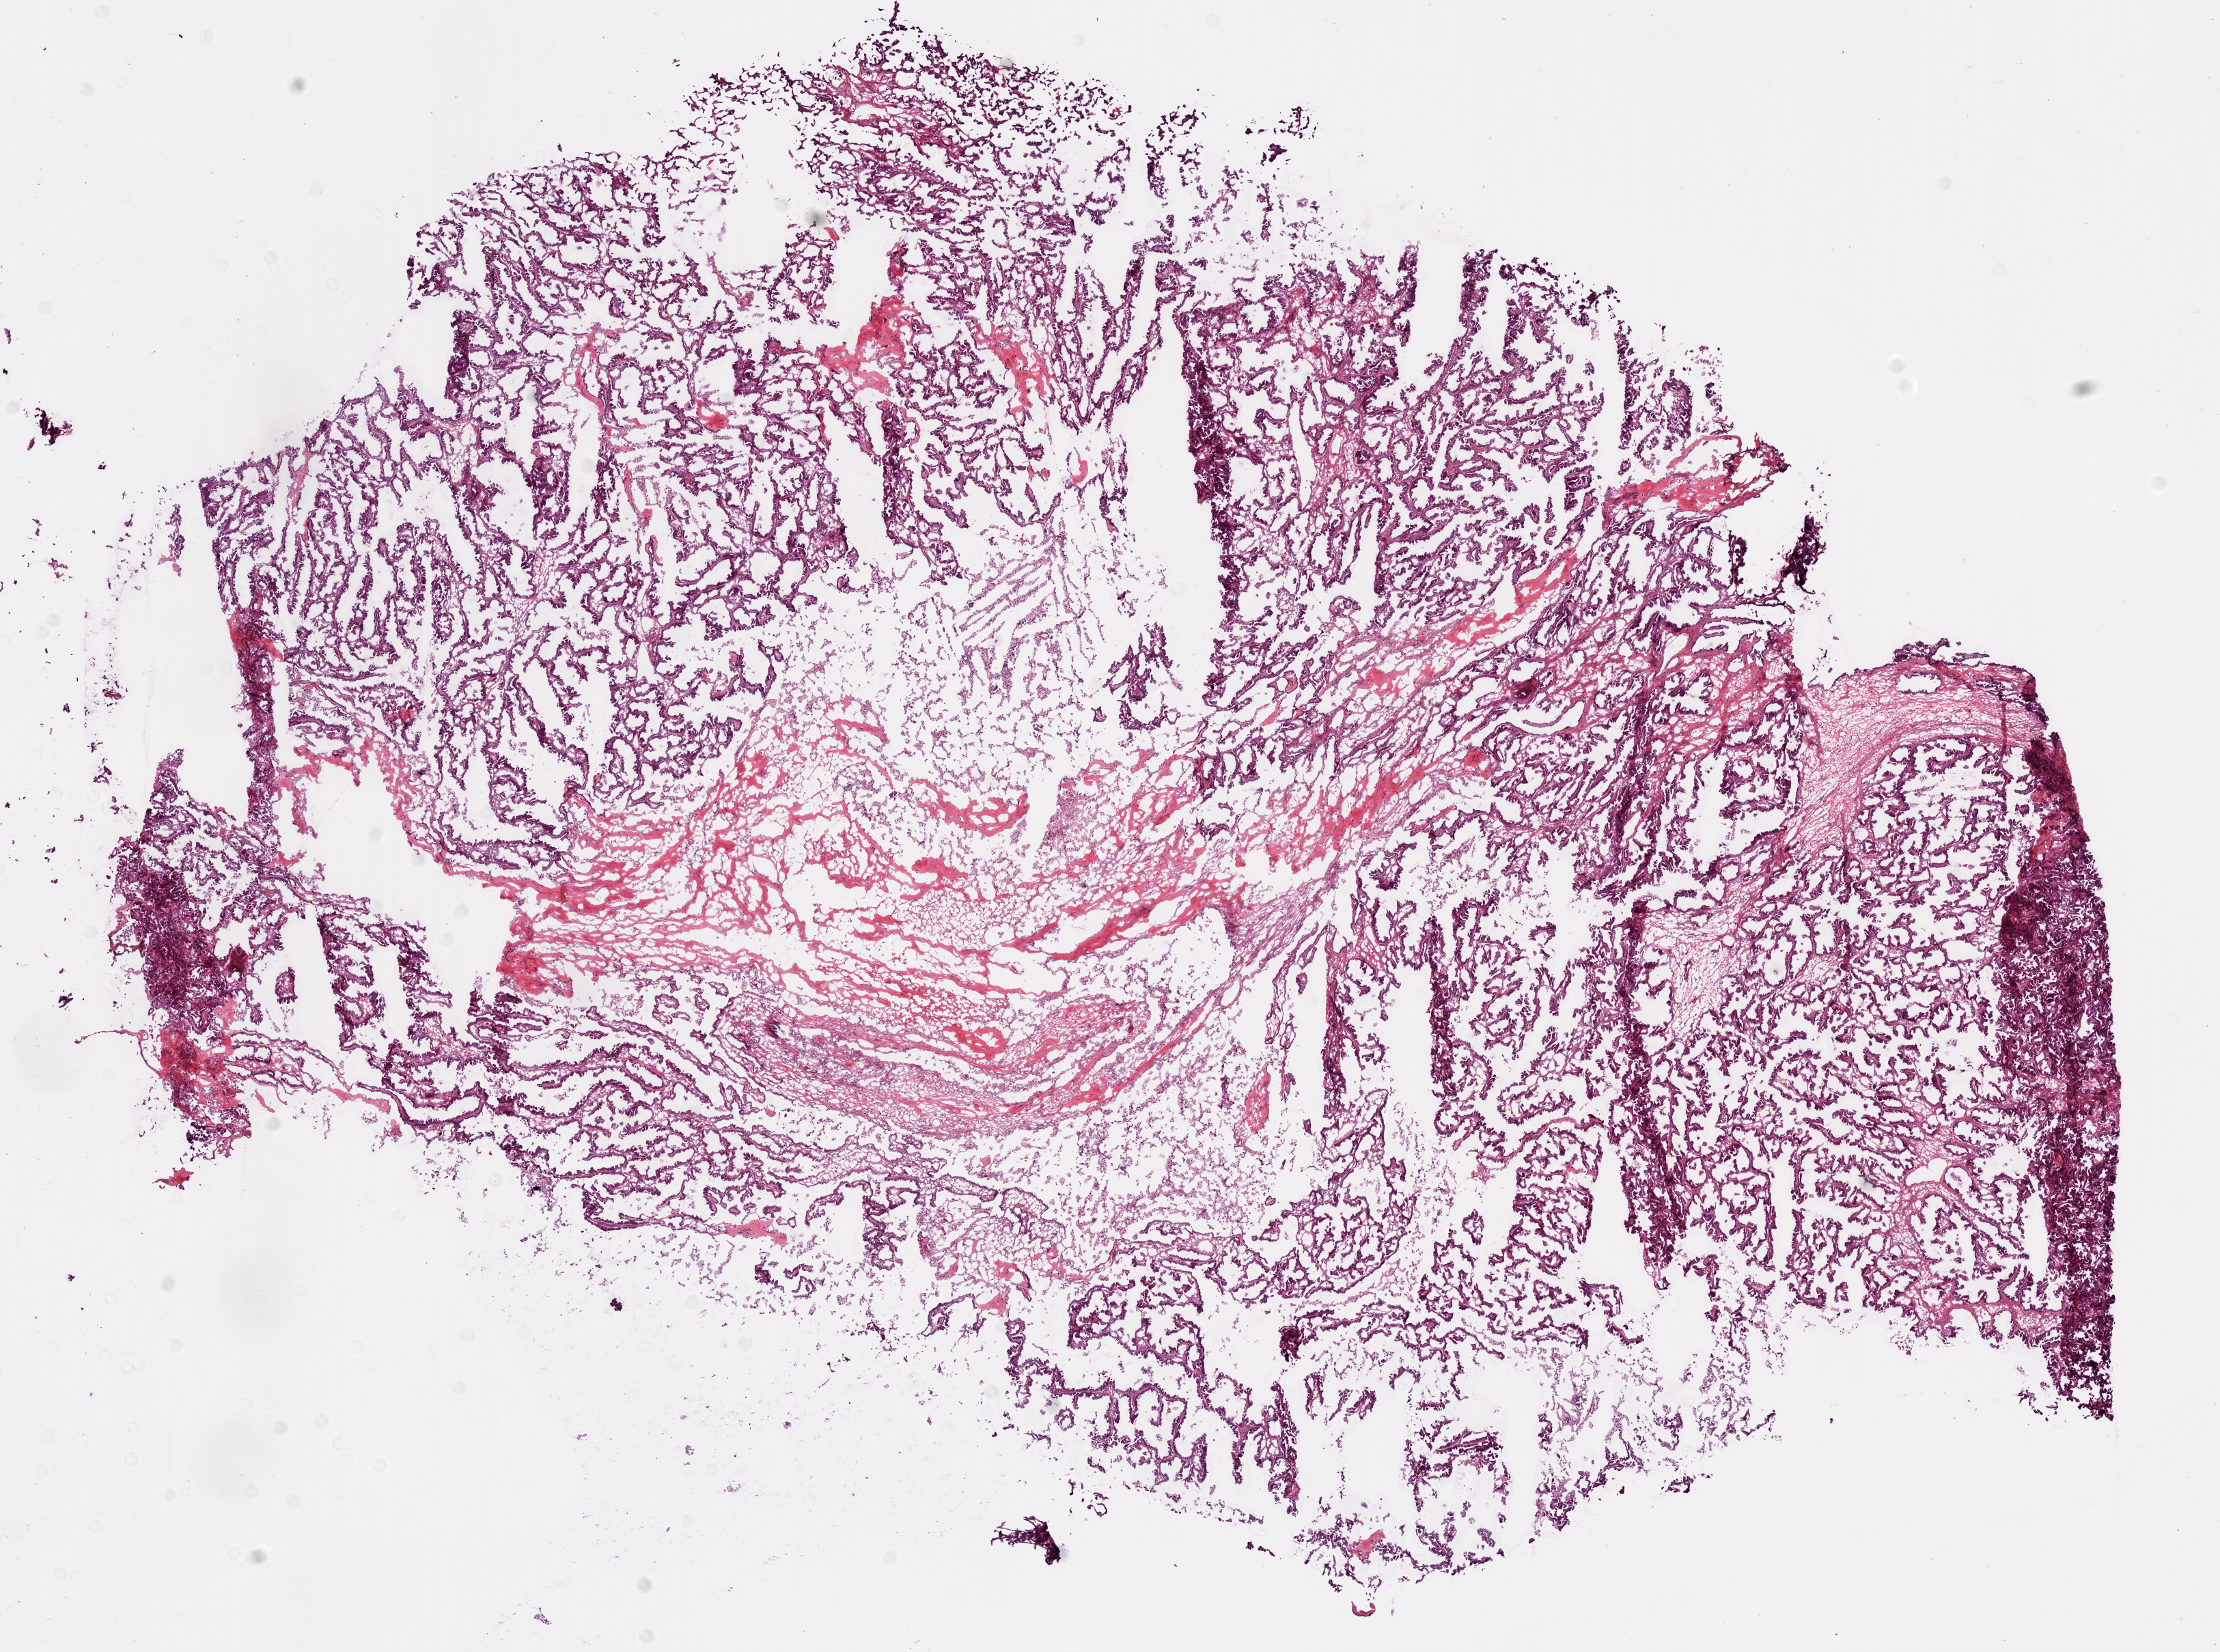
Digitized H&E tissue section (whole slide), shown as a low-resolution overview of the whole scanned area (about 13.0 x 9.7 mm, from a 20x scan), frozen section from the bottom of the tissue portion, sample: primary tumour, ovary. Female patient; age at initial diagnosis 74 years.
Pathologic diagnosis: Serous cystadenocarcinoma, NOS.